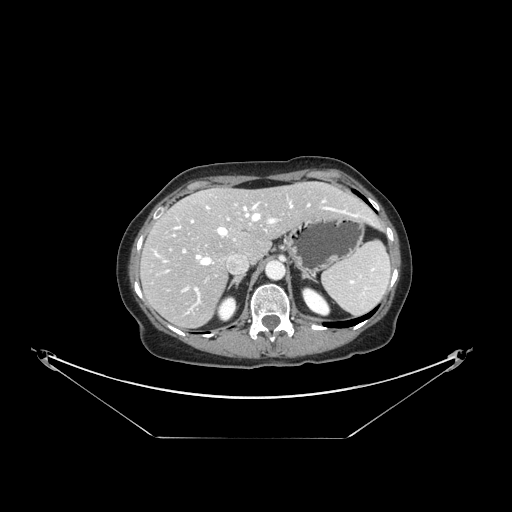
Contrast-enhanced abdominal CT, one axial slice. Reconstruction kernel STANDARD. 120 kVp. Intravenous contrast given. Soft-tissue window (W 400 / L 40 HU). 2.5 mm slice thickness. 512 × 512 image matrix, field of view 500 × 500 mm. Female patient, age 73 years. Case-level facts recorded for this patient, not image findings: diagnosis: colorectal cancer liver metastases, imaged before liver resection; multiple liver metastases: no; largest metastasis: 1 cm; chemotherapy before resection: yes.
Outlined on this slice (manually delineated by an expert):
- hepatic veins: bounding box [x1, y1, x2, y2] px = [163, 200, 361, 265]
- liver: [143, 183, 377, 327]
- planned liver remnant (the part of the liver to remain after resection): [168, 183, 376, 260]
- portal vein (with intrahepatic branches): [173, 218, 277, 304]